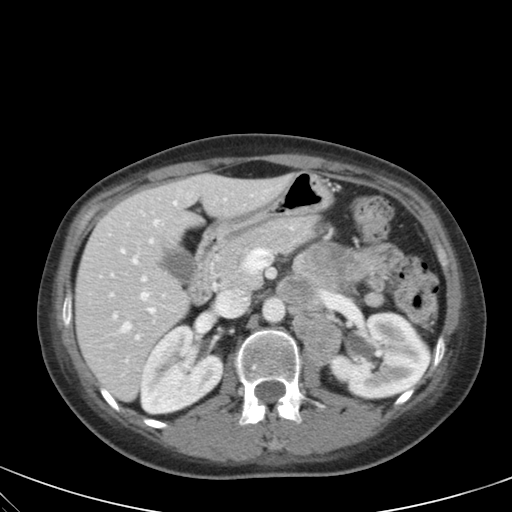
Contrast-enhanced abdominal CT, one axial slice; slice 30 of 59 in the series (ordered by position); intravenous contrast given; soft-tissue window (W 400 / L 40 HU); 4 mm slice thickness; 512 × 512 image matrix. Female patient, age 28 years. From the clinical record (not read from this slice): diagnosis: adrenocortical carcinoma; tumour side: left adrenal; tumour size at pathology: 7 cm; Ki-67 index: 40 %; stage (as recorded): 4.
Annotated regions visible in this slice (semi-automatic segmentation, software-assisted and operator-edited):
- mass: bounding box (x1, y1, x2, y2) in pixels: (295, 244, 355, 293)